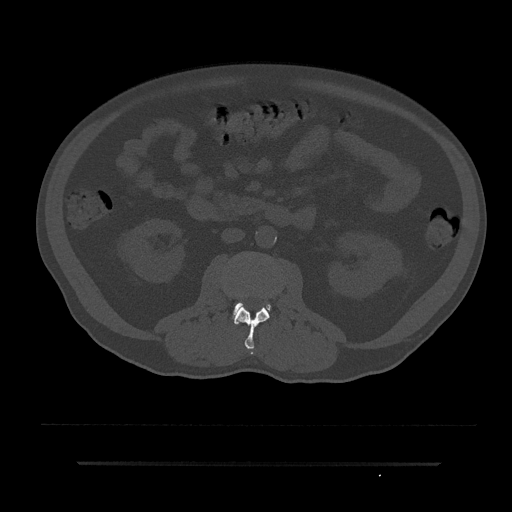
CT including the spine, one axial slice; slice 44 of 797 in the series (ordered by position); reconstruction kernel Br40s/3; 120 kVp; bone window (W 1800 / L 400 HU); 512 × 512 image matrix, field of view 464 × 464 mm. Patient: male, 59 years. Case-level facts recorded for this patient, not image findings: primary cancer: bile ducts.
Structures marked on this image (semi-automatic segmentation, software-assisted and operator-edited):
- L2 vertebra: bounding box (x1, y1, x2, y2) in pixels: (235, 305, 269, 355)
- L3 vertebra: (234, 303, 270, 314)